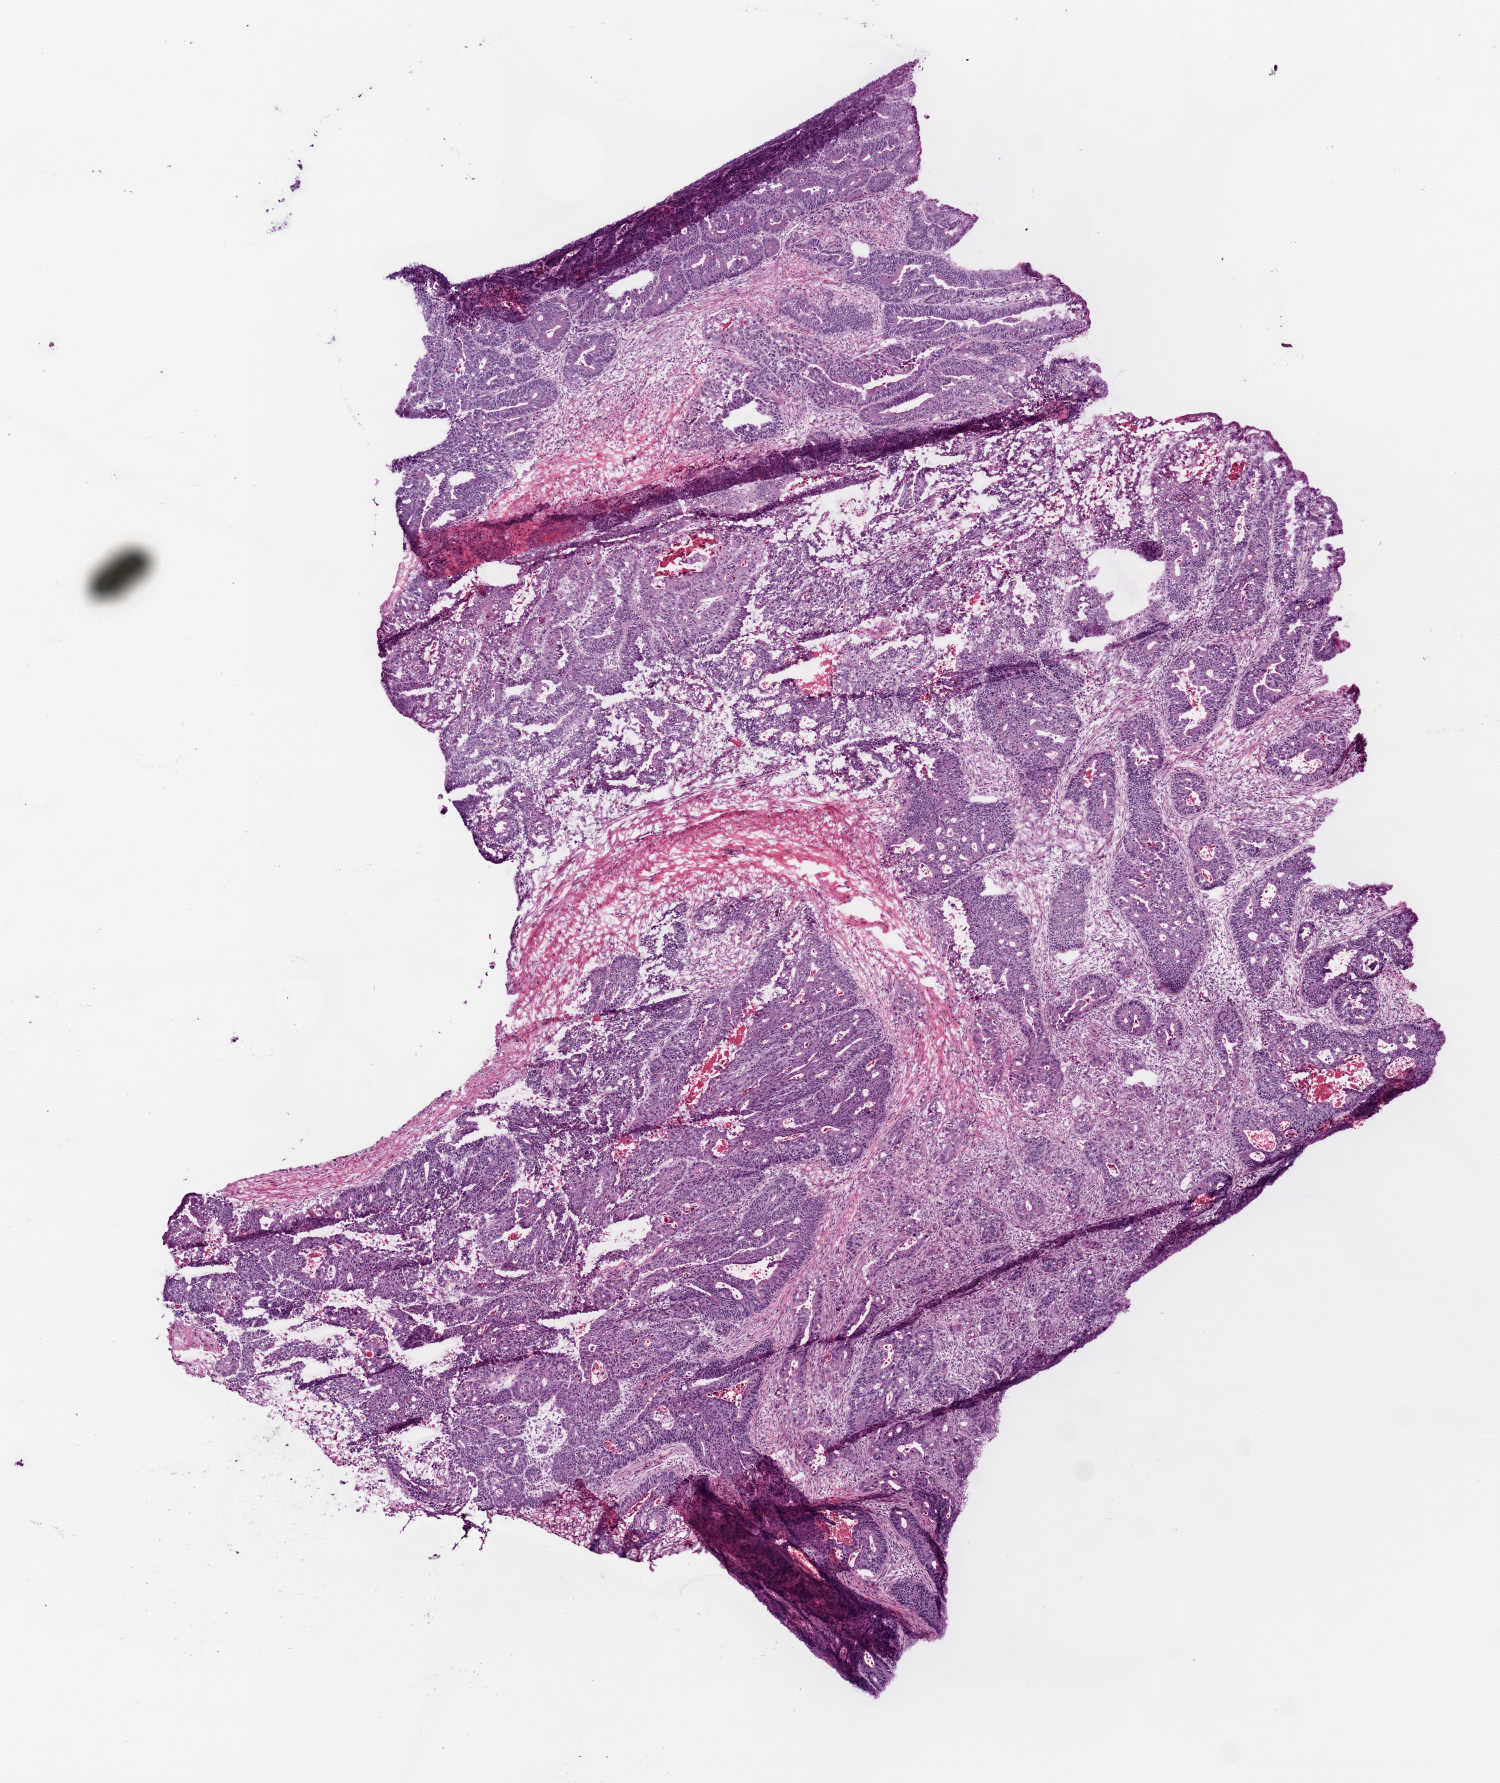
Digitized Hematoxylin and eosin (H&E) stained tissue section (whole slide) — shown as a low-resolution overview of the whole scanned area (about 6.0 x 7.2 mm, acquisition: 20x scan). Frozen section. Primary tumour sample from the colon. Male, age 77 years at initial diagnosis.
Diagnosis: Adenocarcinoma, NOS.